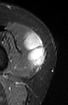
MRI of an extremity soft-tissue mass, one axial slice. Position 36 of 52 along the scan axis. STIR. MR volume resampled by the dataset authors to the PET/CT grid (not the native acquisition matrix). 68 × 105 image matrix. Female patient. From the clinical record (not read from this slice): histological type: spindle cell suggestive of biphasic synovial sarcoma; grade: intermediate; site of the primary tumour: left knee.
Annotated regions visible in this slice (expert contour drawn on MRI and transferred to this co-registered scan by the dataset authors):
- gross tumour volume including surrounding oedema: bounding box [x1, y1, x2, y2] px = [23, 31, 45, 67]
- gross tumour volume (mass): [23, 31, 45, 67]